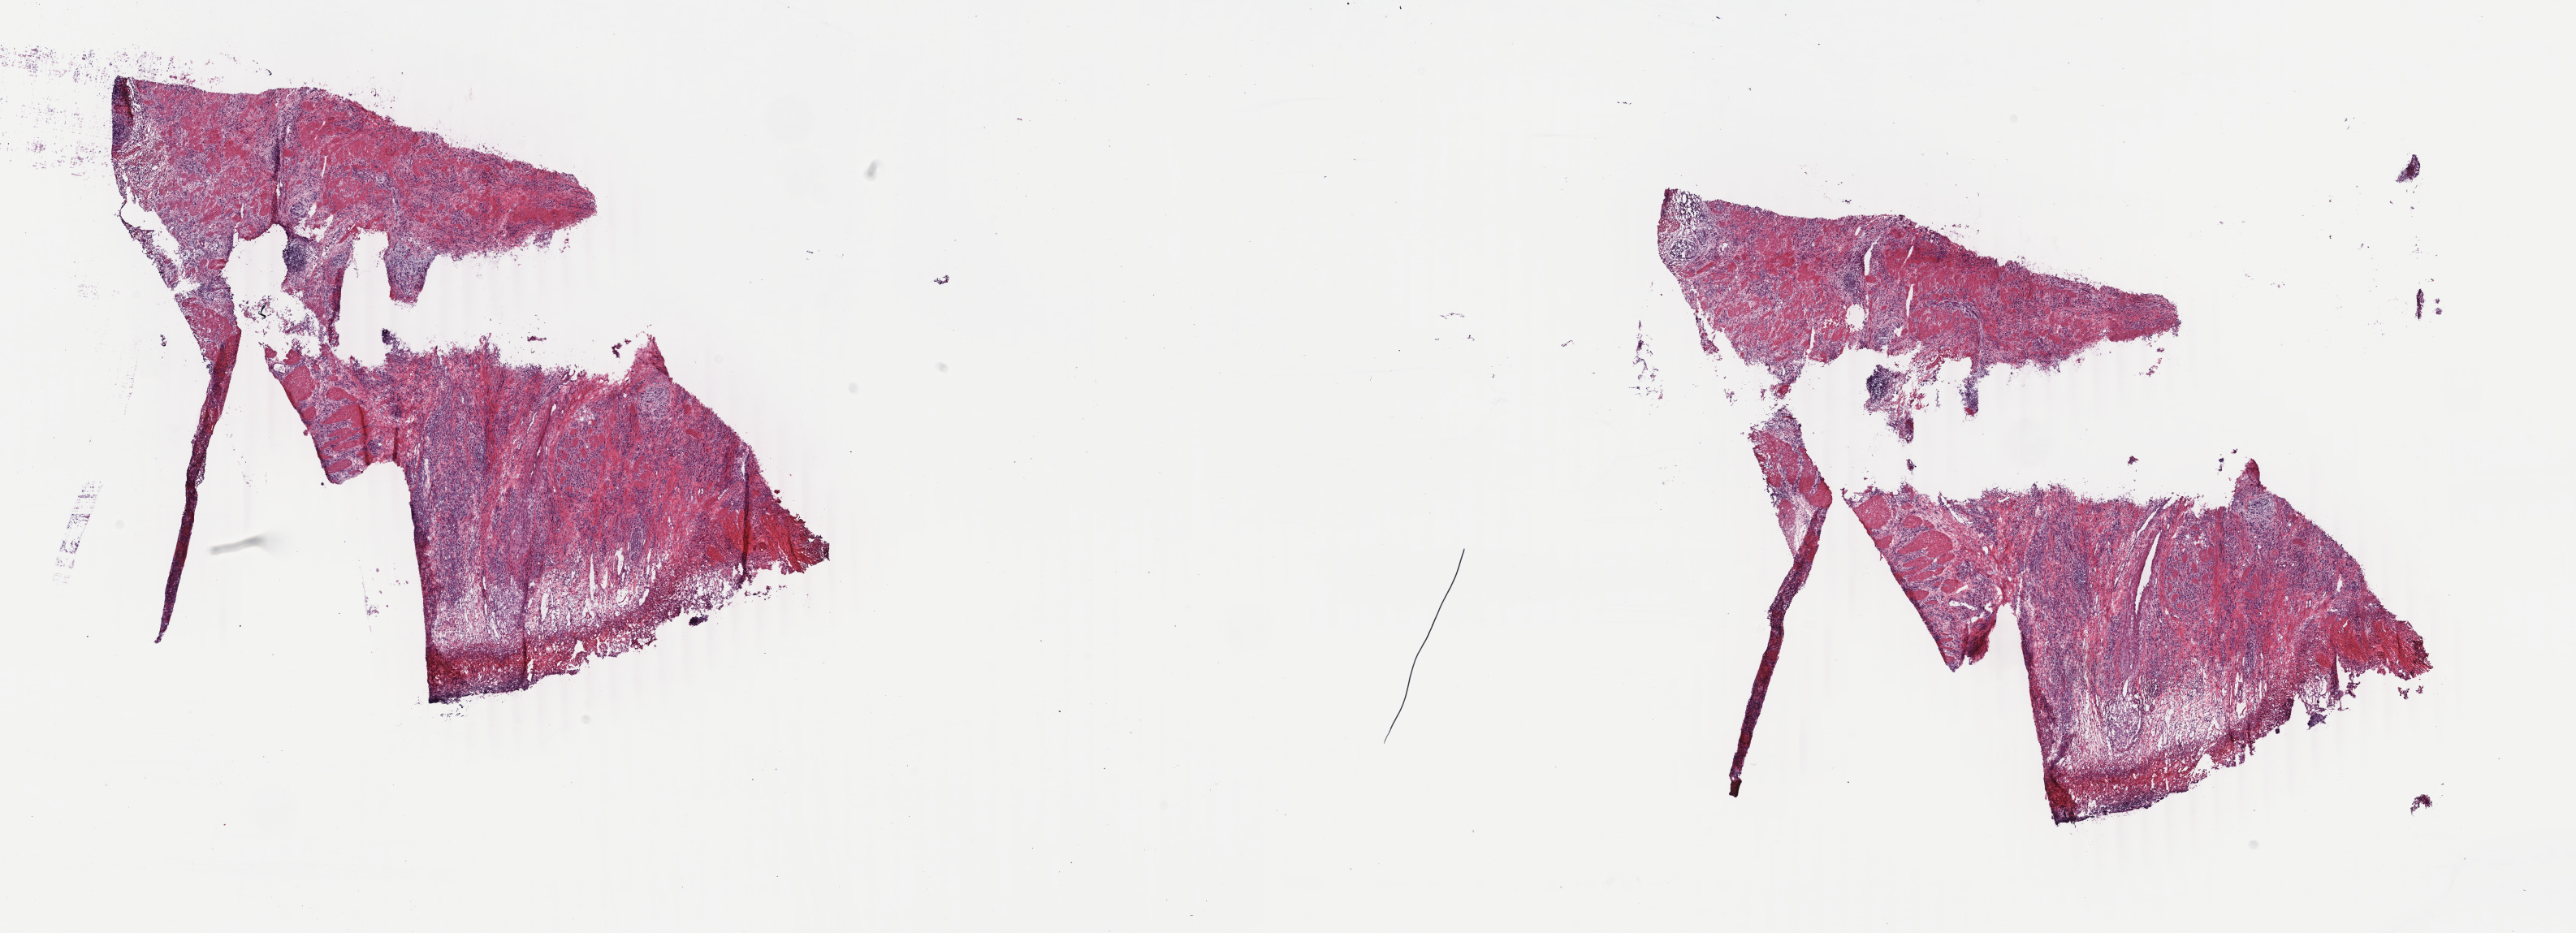
Digitized H&E tissue section (whole slide), a low-resolution overview of the entire scanned area, about 25.2 x 9.1 mm, frozen section from the top of the tissue portion, sample: primary tumour, stomach. Male, age 70 years at initial diagnosis. Composition of this section per pathologist review: tumour cells 95%, tumour nuclei 70%.
Histologic diagnosis: Carcinoma, diffuse type (gastric antrum).